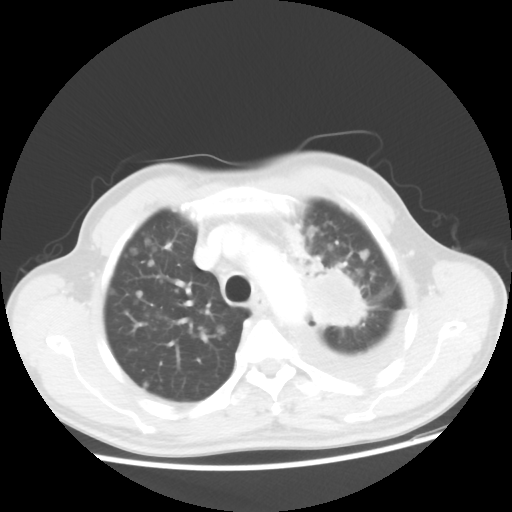
Chest CT, one axial slice; position 37 of 48 along the scan axis; 100 kVp; lung window (W 1500 / L -600 HU); 5 mm slice thickness; 512 × 512 image matrix, field of view 362 × 362 mm. Male patient, age 55 years. Case-level facts recorded for this patient, not image findings: clinical TNM (as recorded): T2 N3 M1a; histopathological grade: G3.
Structures marked on this image (rectangle marked by the reading radiologist):
- lung tumour (recorded histology: squamous cell carcinoma): bounding box <306,253,361,356> (left, top, right, bottom; pixels)